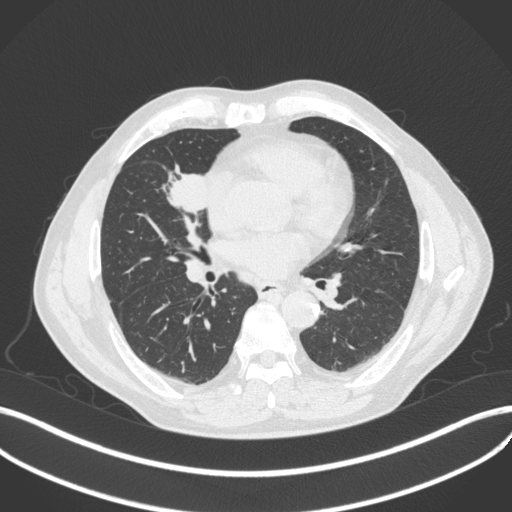
Chest CT, one axial slice. Slice 193 of 429 in the series (ordered by position). Lung window (W 1500 / L -600 HU). 1 mm slice thickness. 512 × 512 image matrix, field of view 400 × 400 mm. Patient: male, 61 years. Case-level facts recorded for this patient, not image findings: clinical TNM (as recorded): T2b N1 M0.
Structures marked on this image (bounding box drawn by a radiologist):
- lung tumour (recorded histology: squamous cell carcinoma): bounding box <161,161,214,221> (left, top, right, bottom; pixels)